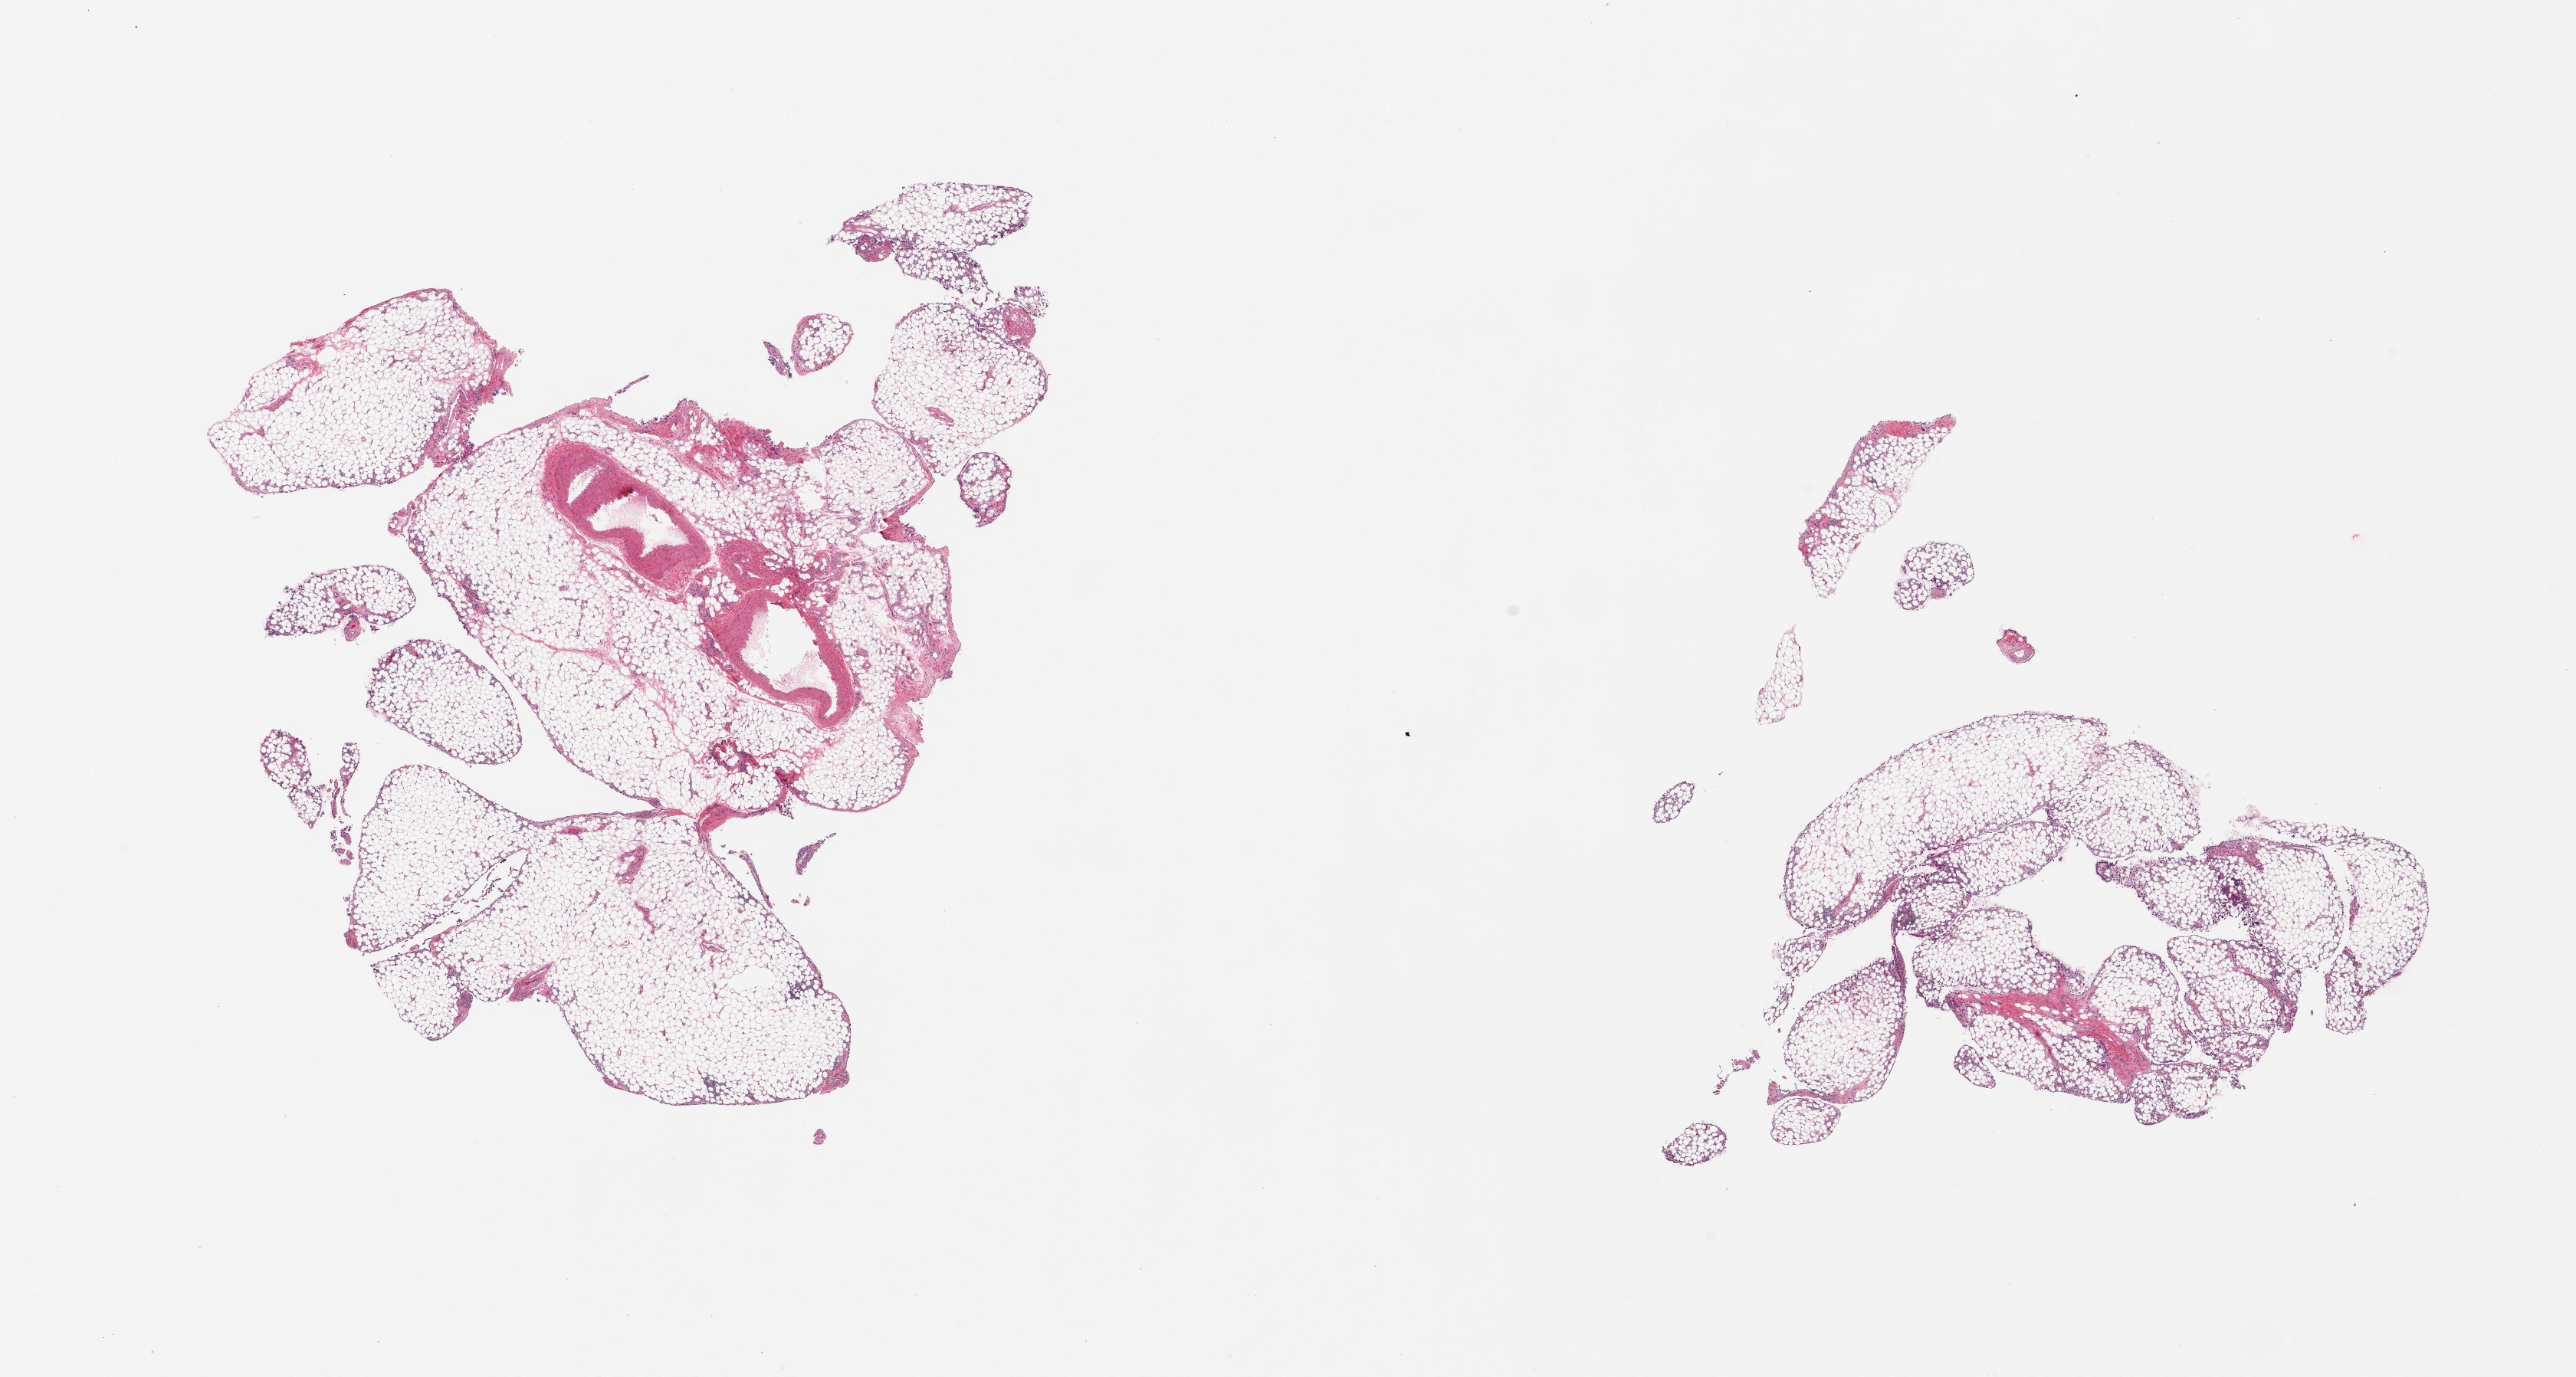
Haematoxylin and eosin whole-slide image, low-resolution overview of the scanned area, about 26.6 x 14.2 mm, PAXgene-fixed, paraffin-embedded tissue, target tissue: omentum, donor tissue sample. Donor sex: male.
Pathologist's review note for this sample: 2 pieces; foci of lymphoid cells; large blood vessel in 1 piece (10%).